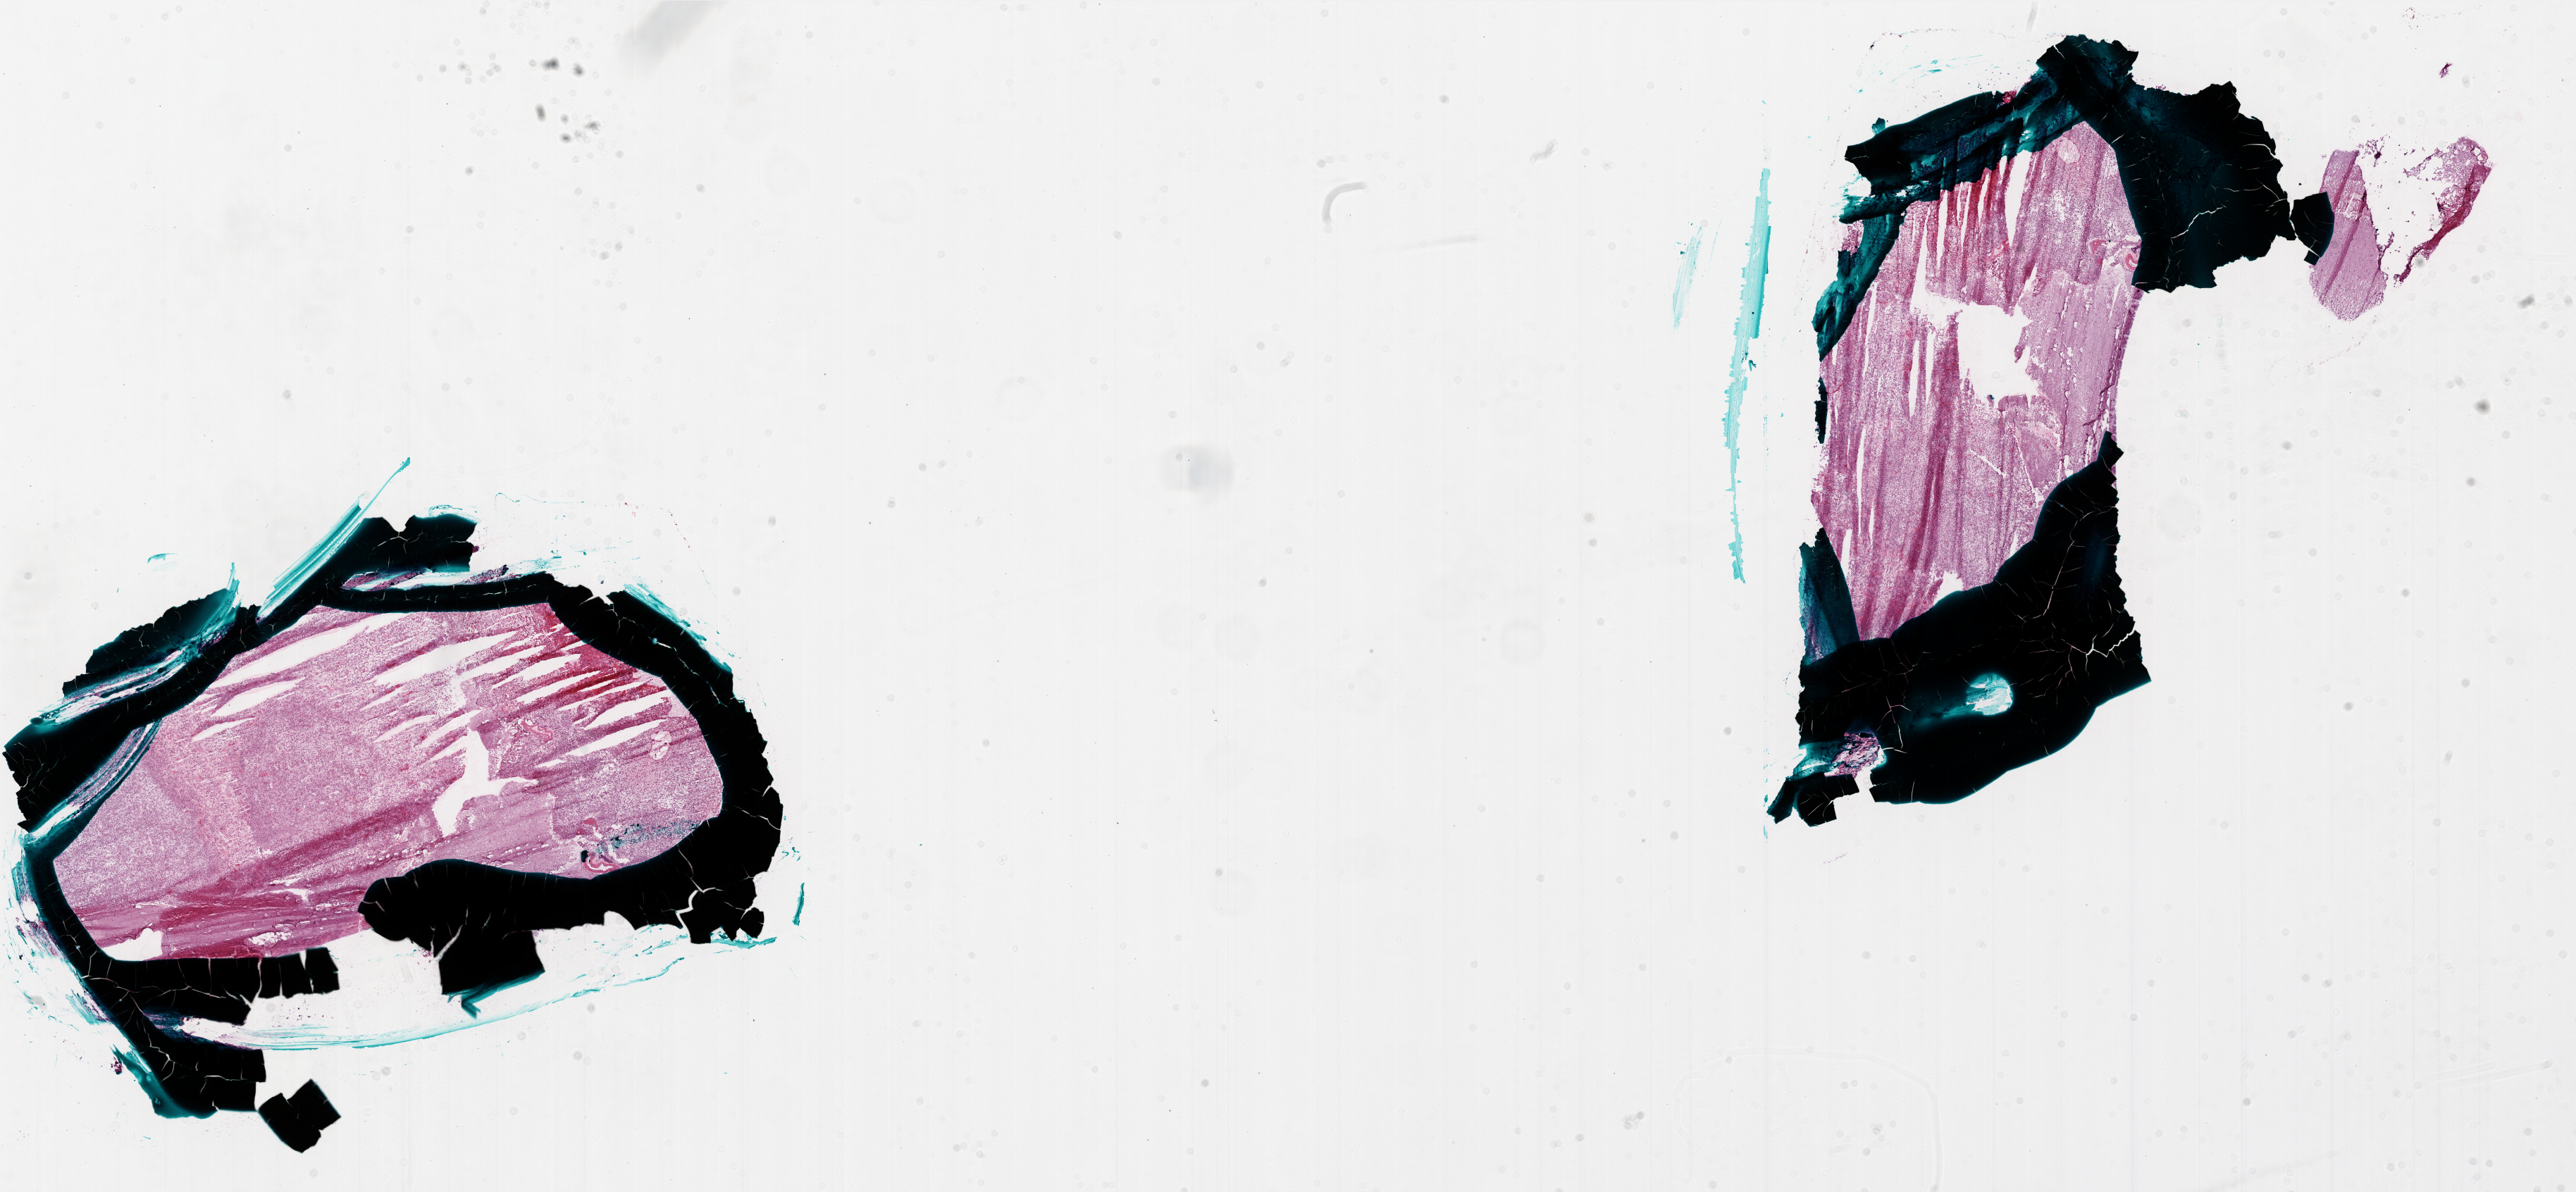
Digitized Hematoxylin and eosin (H&E) stained tissue section (whole slide), whole scanned area (about 29.4 x 13.6 mm) shown as a low-resolution overview, frozen section, primary tumour sample from the brain. Male, age 64 years at initial diagnosis.
Histologic diagnosis: Glioblastoma.